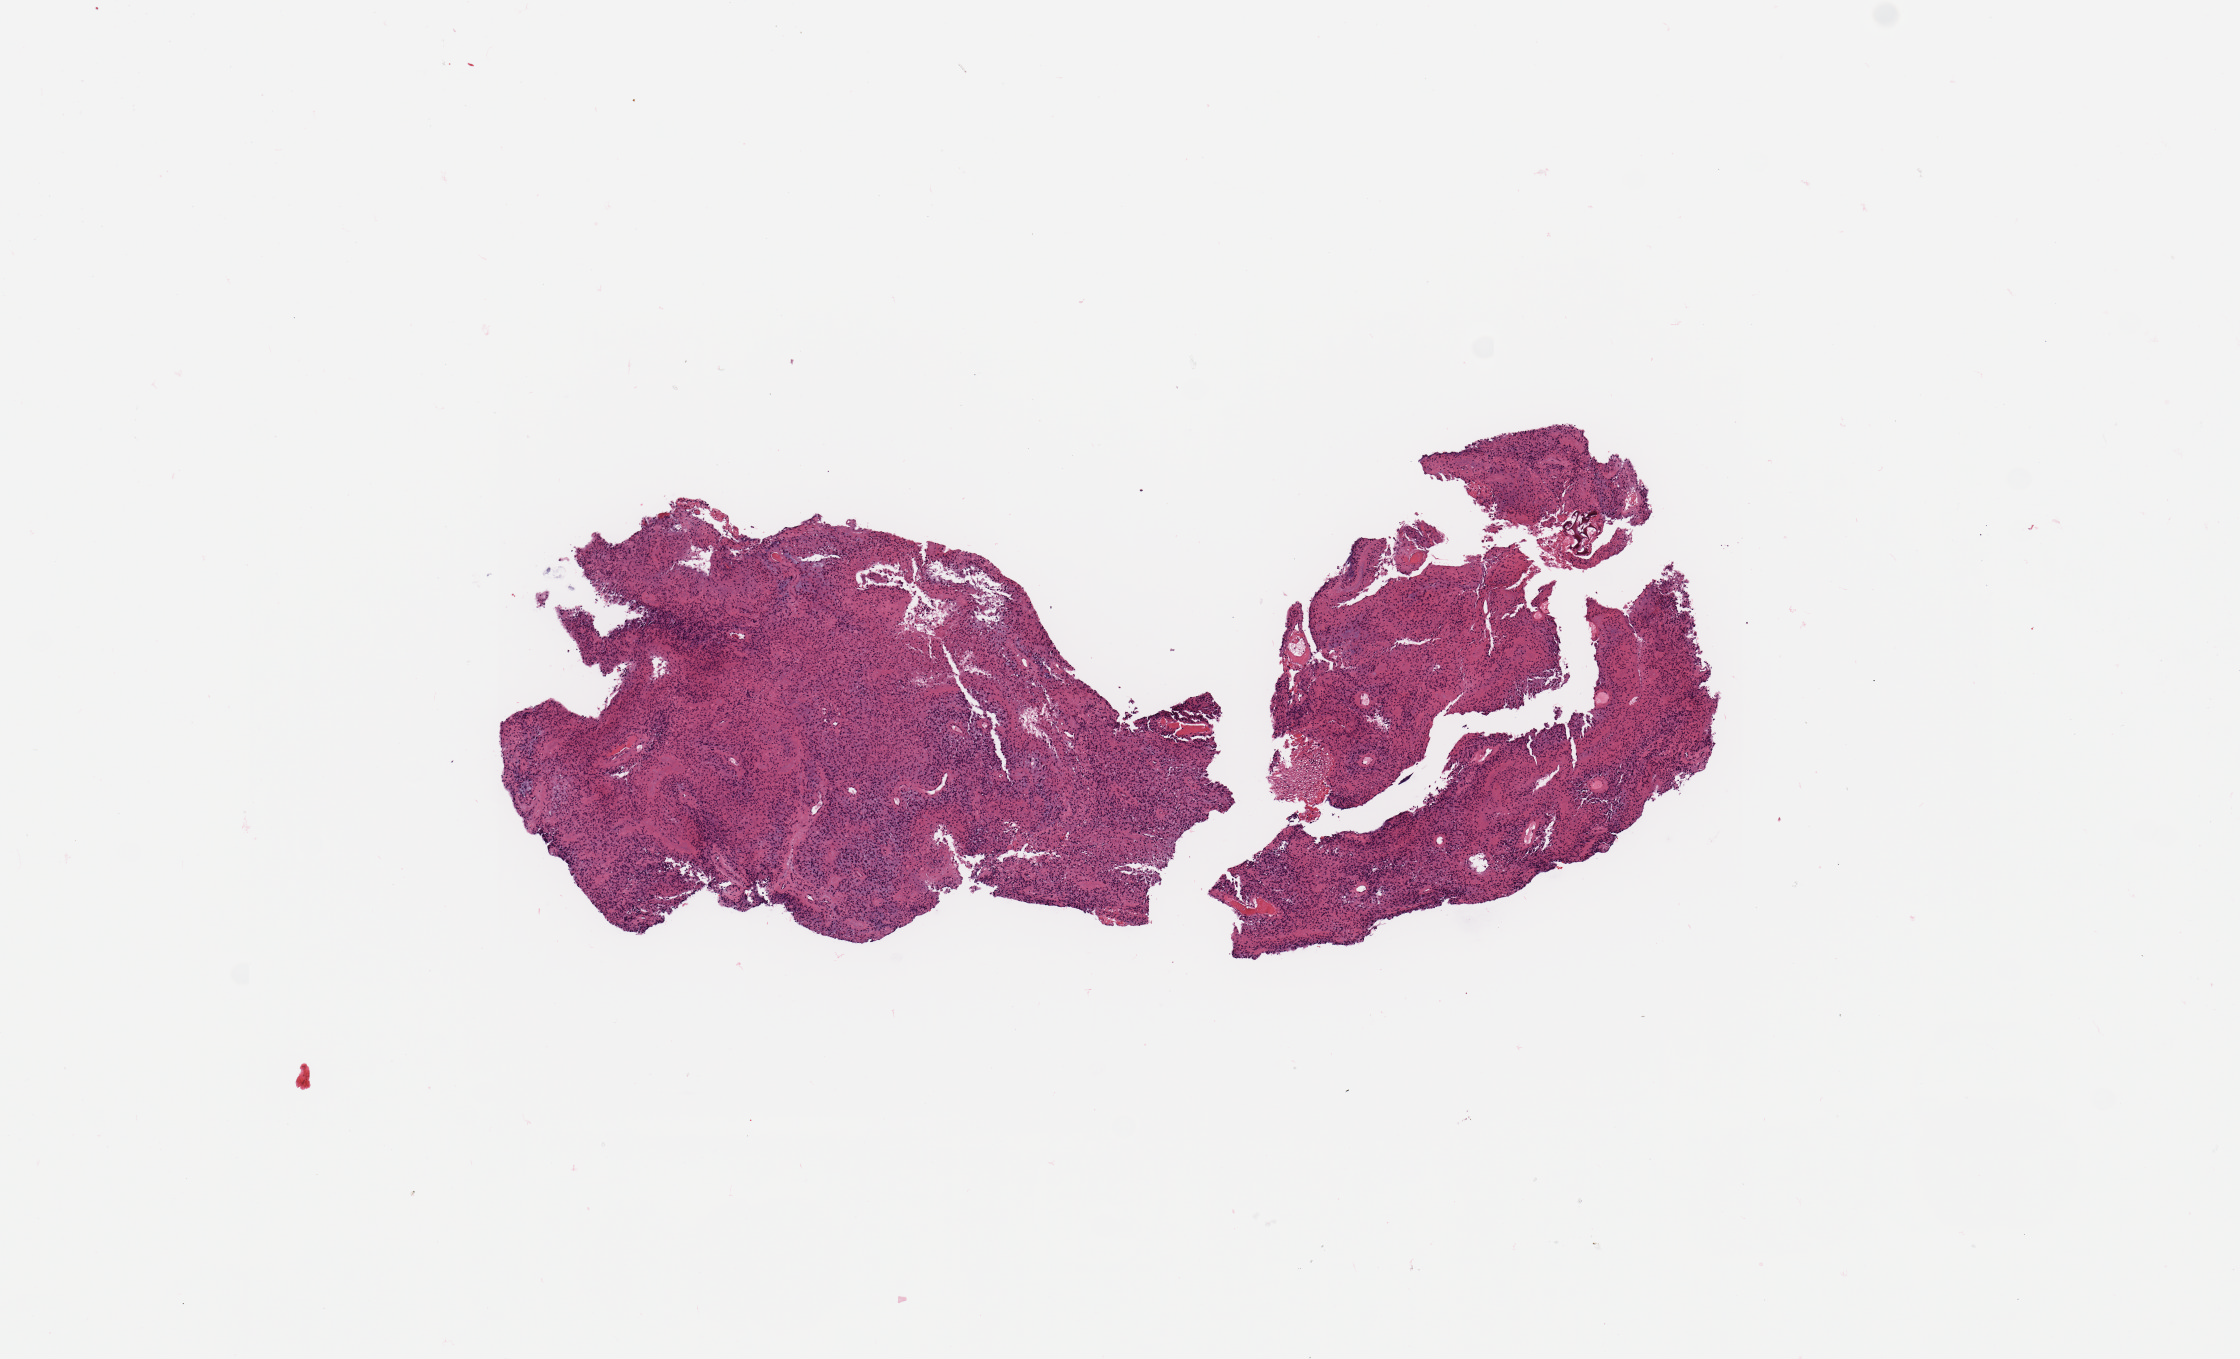
Digitized H&E-stained tissue section (whole slide) — shown as a low-resolution overview of the whole scanned area (about 8.9 x 5.4 mm, from a 20x scan); tumour tissue sample, sampled site: occipital cortex. Male, 71 y/o. Slide review estimates, as recorded: tumour nuclei 85%, necrosis 2%.
- diagnosis: Glioblastoma
- primary tumour site (as recorded): occipital lobe